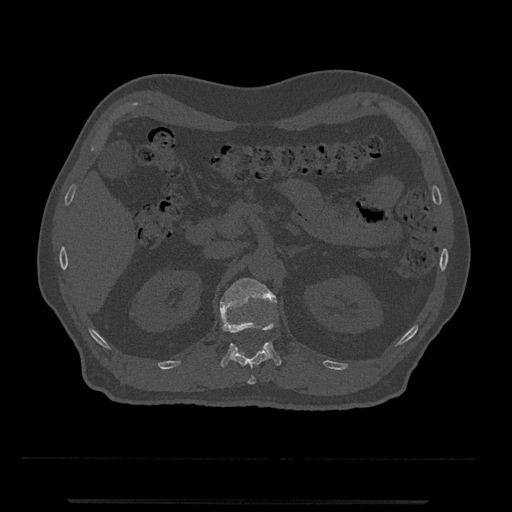
CT including the spine, one axial slice; slice 368 of 797 in the series (ordered by position); reconstruction kernel Br40s/3; 120 kVp; bone window (W 1800 / L 400 HU); 0.5 mm slice thickness; 512 × 512 image matrix, field of view 419 × 419 mm. Patient: male, 63 years. From the clinical record (not read from this slice): primary cancer: prostate.
Structures marked on this image (semi-automatic segmentation, software-assisted and operator-edited):
- L1 vertebra: bounding box <220,278,281,368> (left, top, right, bottom; pixels)
- T12 vertebra: <231,348,270,385>